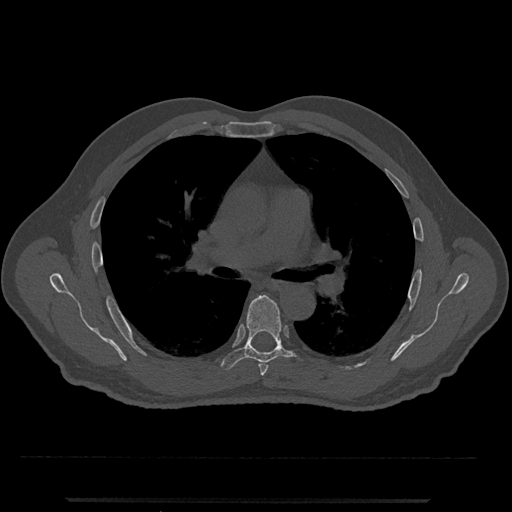
CT including the spine, one axial slice; position 746 of 797 along the scan axis; reconstruction kernel Br40s/3; bone window (W 1800 / L 400 HU); 512 × 512 image matrix, field of view 419 × 419 mm. Male patient, age 63 years. From the clinical record (not read from this slice): primary cancer: prostate.
Structures marked on this image (semi-automatically segmented with operator editing):
- T5 vertebra: bounding box [x1, y1, x2, y2] px = [259, 362, 268, 376]
- T6 vertebra: [221, 295, 304, 370]